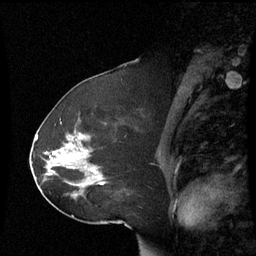
Breast MRI (dynamic contrast-enhanced), one sagittal slice; position 36 of 60 along the scan axis; dynamic contrast-enhanced series, image 2 of 3 at this slice position (ordered by acquisition); 1.5 T; TE 4.2 ms, TR 8.9 ms; 256 × 256 image matrix. Patient: female, 51 years. From the clinical record (not read from this slice): setting: breast cancer imaged before/during neoadjuvant chemotherapy; receptor status: HR-positive, HER2-negative.
Structures marked on this image (semi-automatic segmentation, software-assisted and operator-edited):
- analysis volume of interest (the breast-tissue region the enhancement analysis was run in; not a lesion): bounding box <42,121,106,199> (left, top, right, bottom; pixels)
- tumour enhancement mask (voxels above the 70 % enhancement threshold inside the analysis volume of interest): <93,170,103,184>